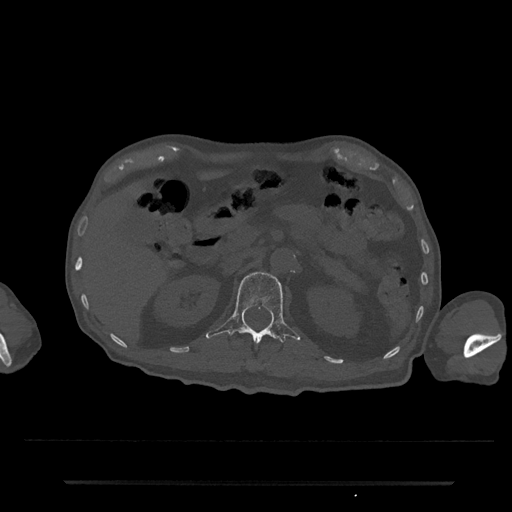
CT including the spine, one axial slice. Position 137 of 797 along the scan axis. Reconstruction kernel Br40s/3. Bone window (W 1800 / L 400 HU). 512 × 512 image matrix, field of view 427 × 427 mm. Male patient, age 74 years. Case-level facts recorded for this patient, not image findings: primary cancer: prostate.
Outlined on this slice (semi-automatically segmented with operator editing):
- L1 vertebra: bounding box (x1, y1, x2, y2) in pixels: (206, 272, 300, 343)